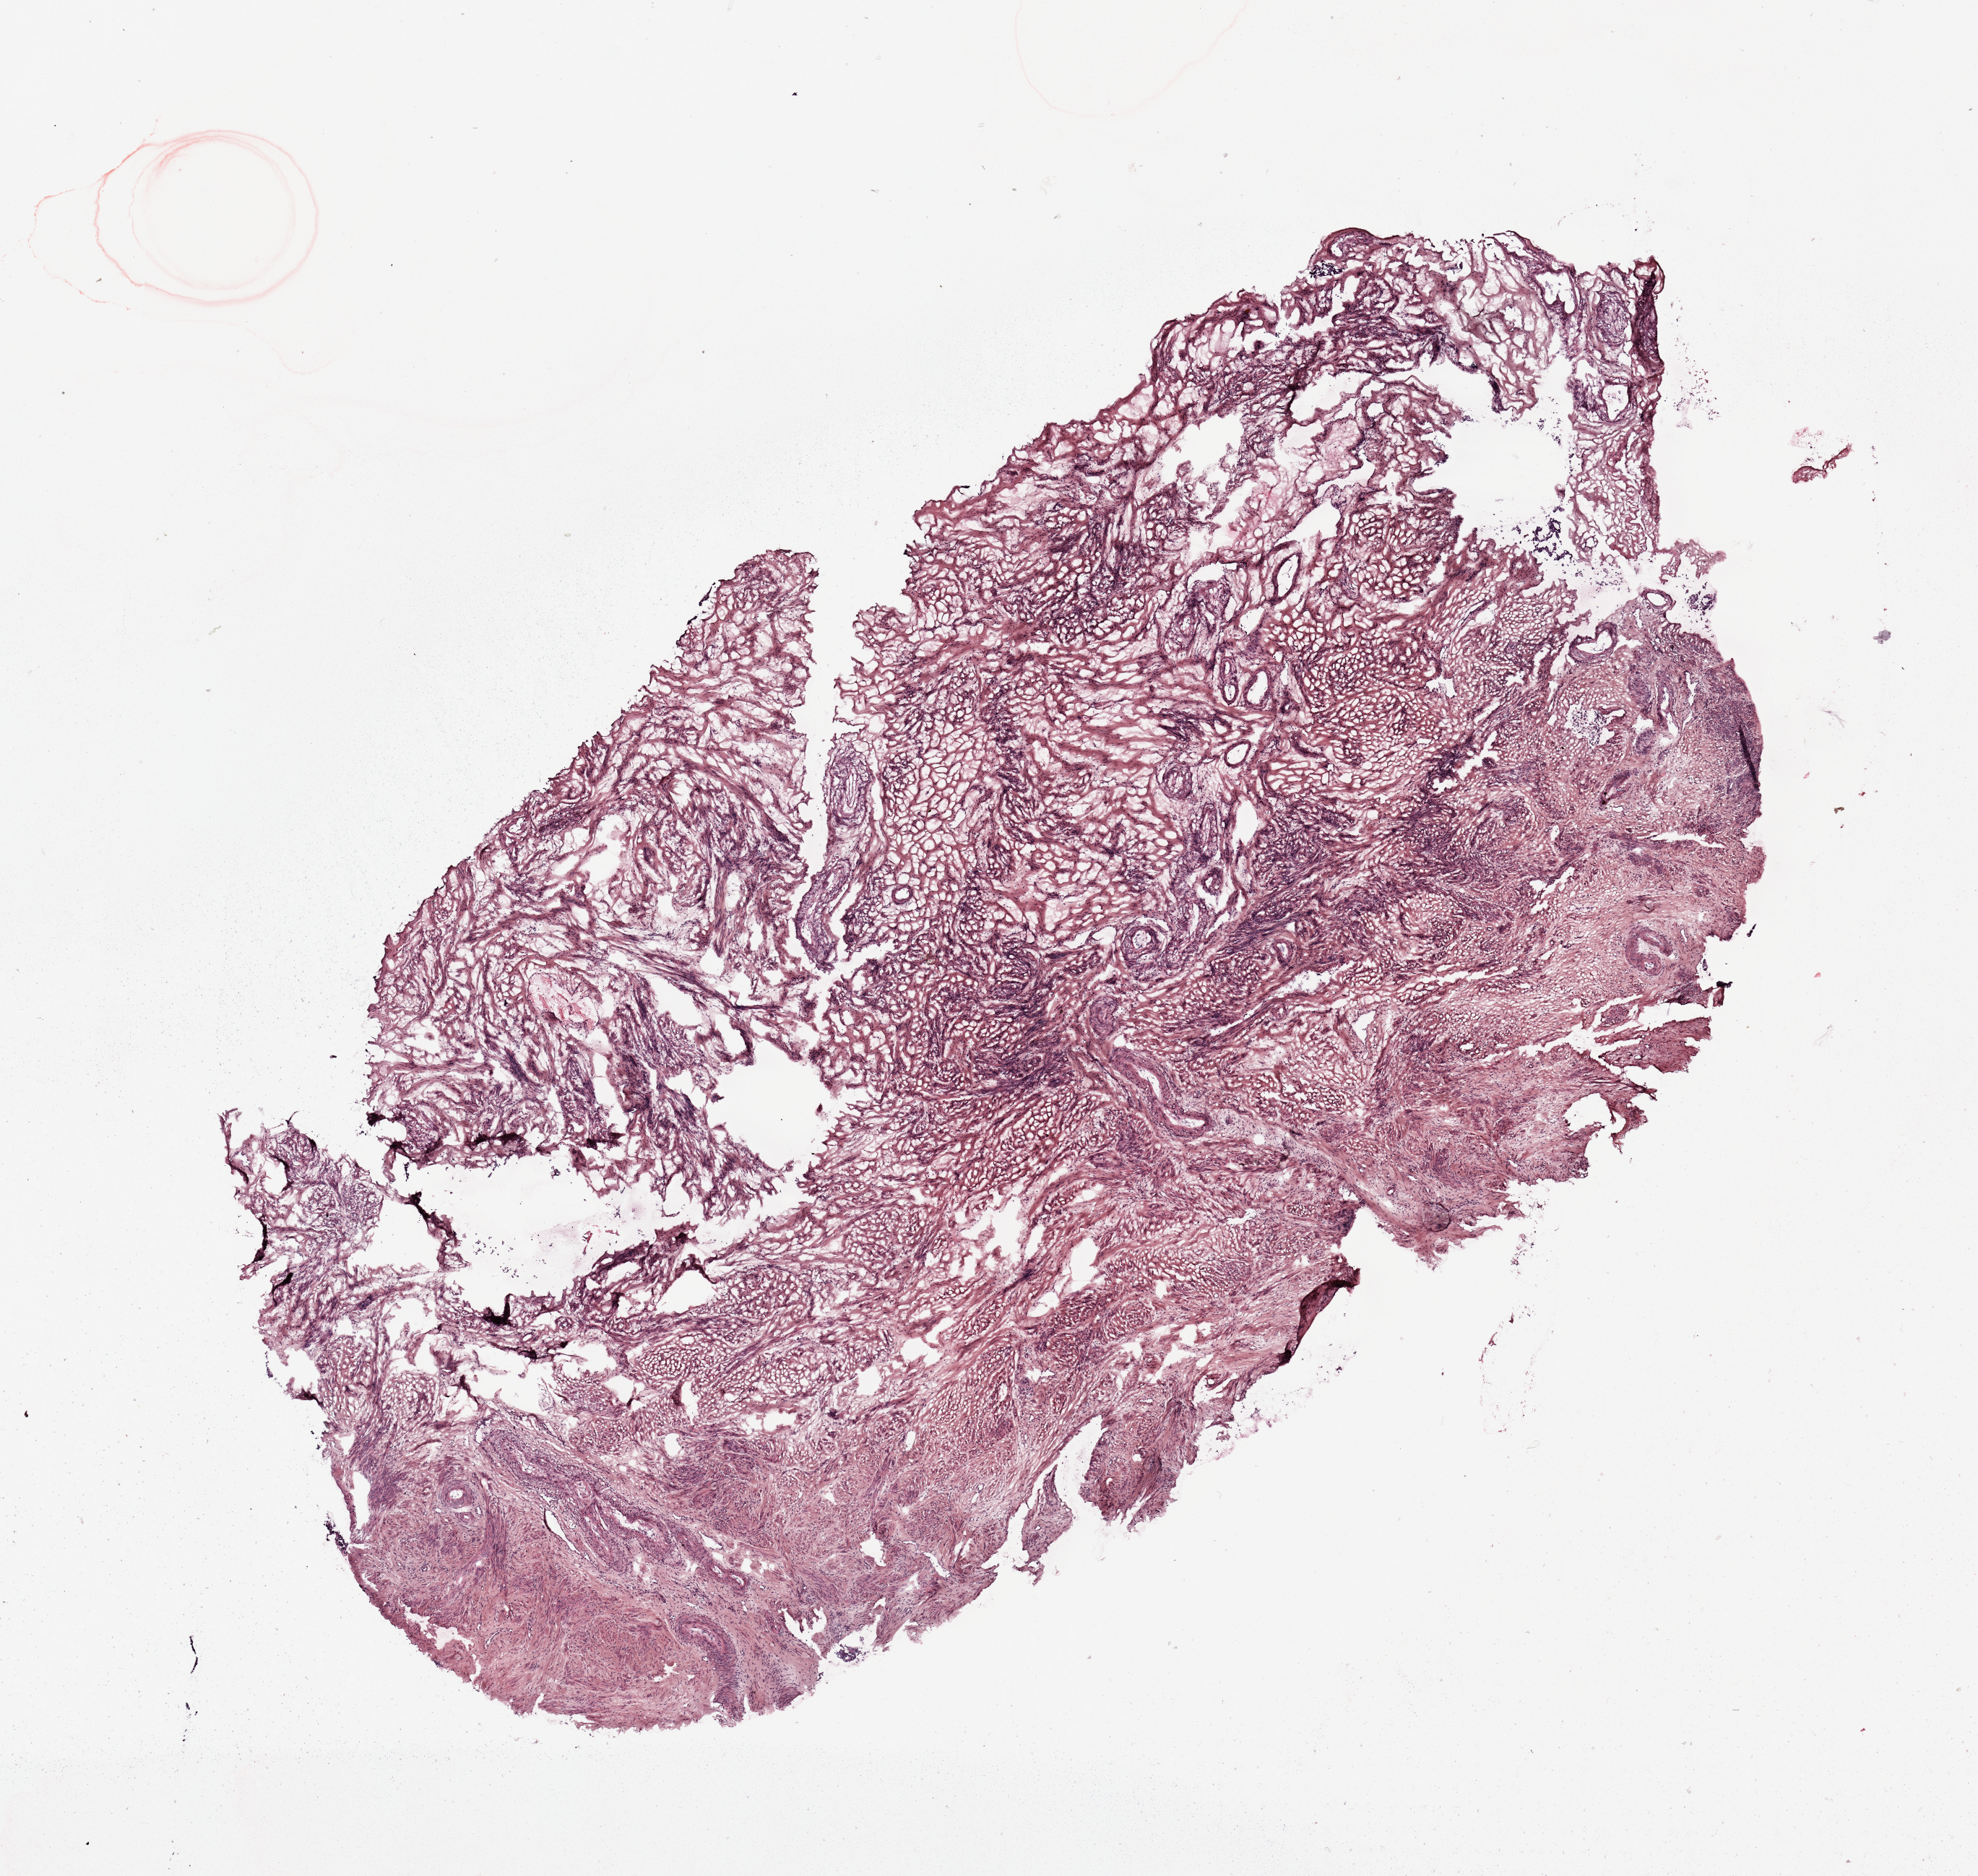
H&E-stained whole-slide image — shown as a low-resolution overview of the whole scanned area (about 10.8 x 10.3 mm); normal (non-tumour) tissue sample, uterus. Patient: female, age 64 years.
* this section: normal (non-tumour) tissue from the same patient
* patient diagnosis: Endometrioid adenocarcinoma, NOS